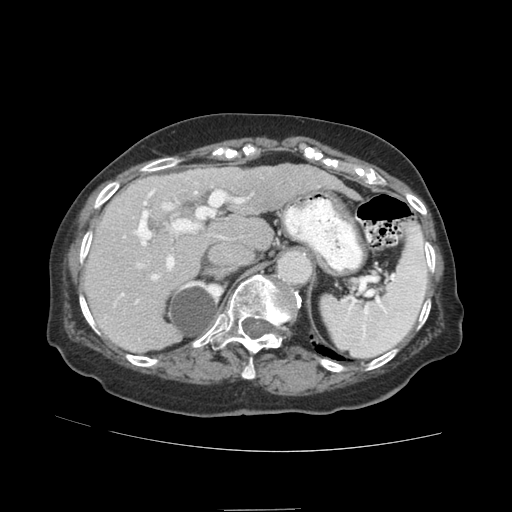
Contrast-enhanced abdominal CT (liver protocol), one axial slice; position 60 of 89 along the scan axis; reconstruction kernel STANDARD; soft-tissue window (W 400 / L 40 HU); 2.5 mm slice thickness; 512 × 512 image matrix, field of view 360 × 360 mm. From the clinical record (not read from this slice): diagnosis: hepatocellular carcinoma (patient treated with transarterial chemoembolisation; whether this scan precedes or follows treatment is not stated here); TNM stage (as recorded): Stage-II; Child-Pugh class: A; tumour nodularity: multinodular.
Annotated regions visible in this slice (semi-automatic segmentation, software-assisted and operator-edited):
- liver parenchyma outside the tumour (the mass and vessels are separate outlines, so this box may not span the whole liver): box from (x=84, y=164) to (x=328, y=352) px
- mass: (x=241, y=167)–(x=280, y=189)
- liver vessels: (x=113, y=172)–(x=253, y=307)